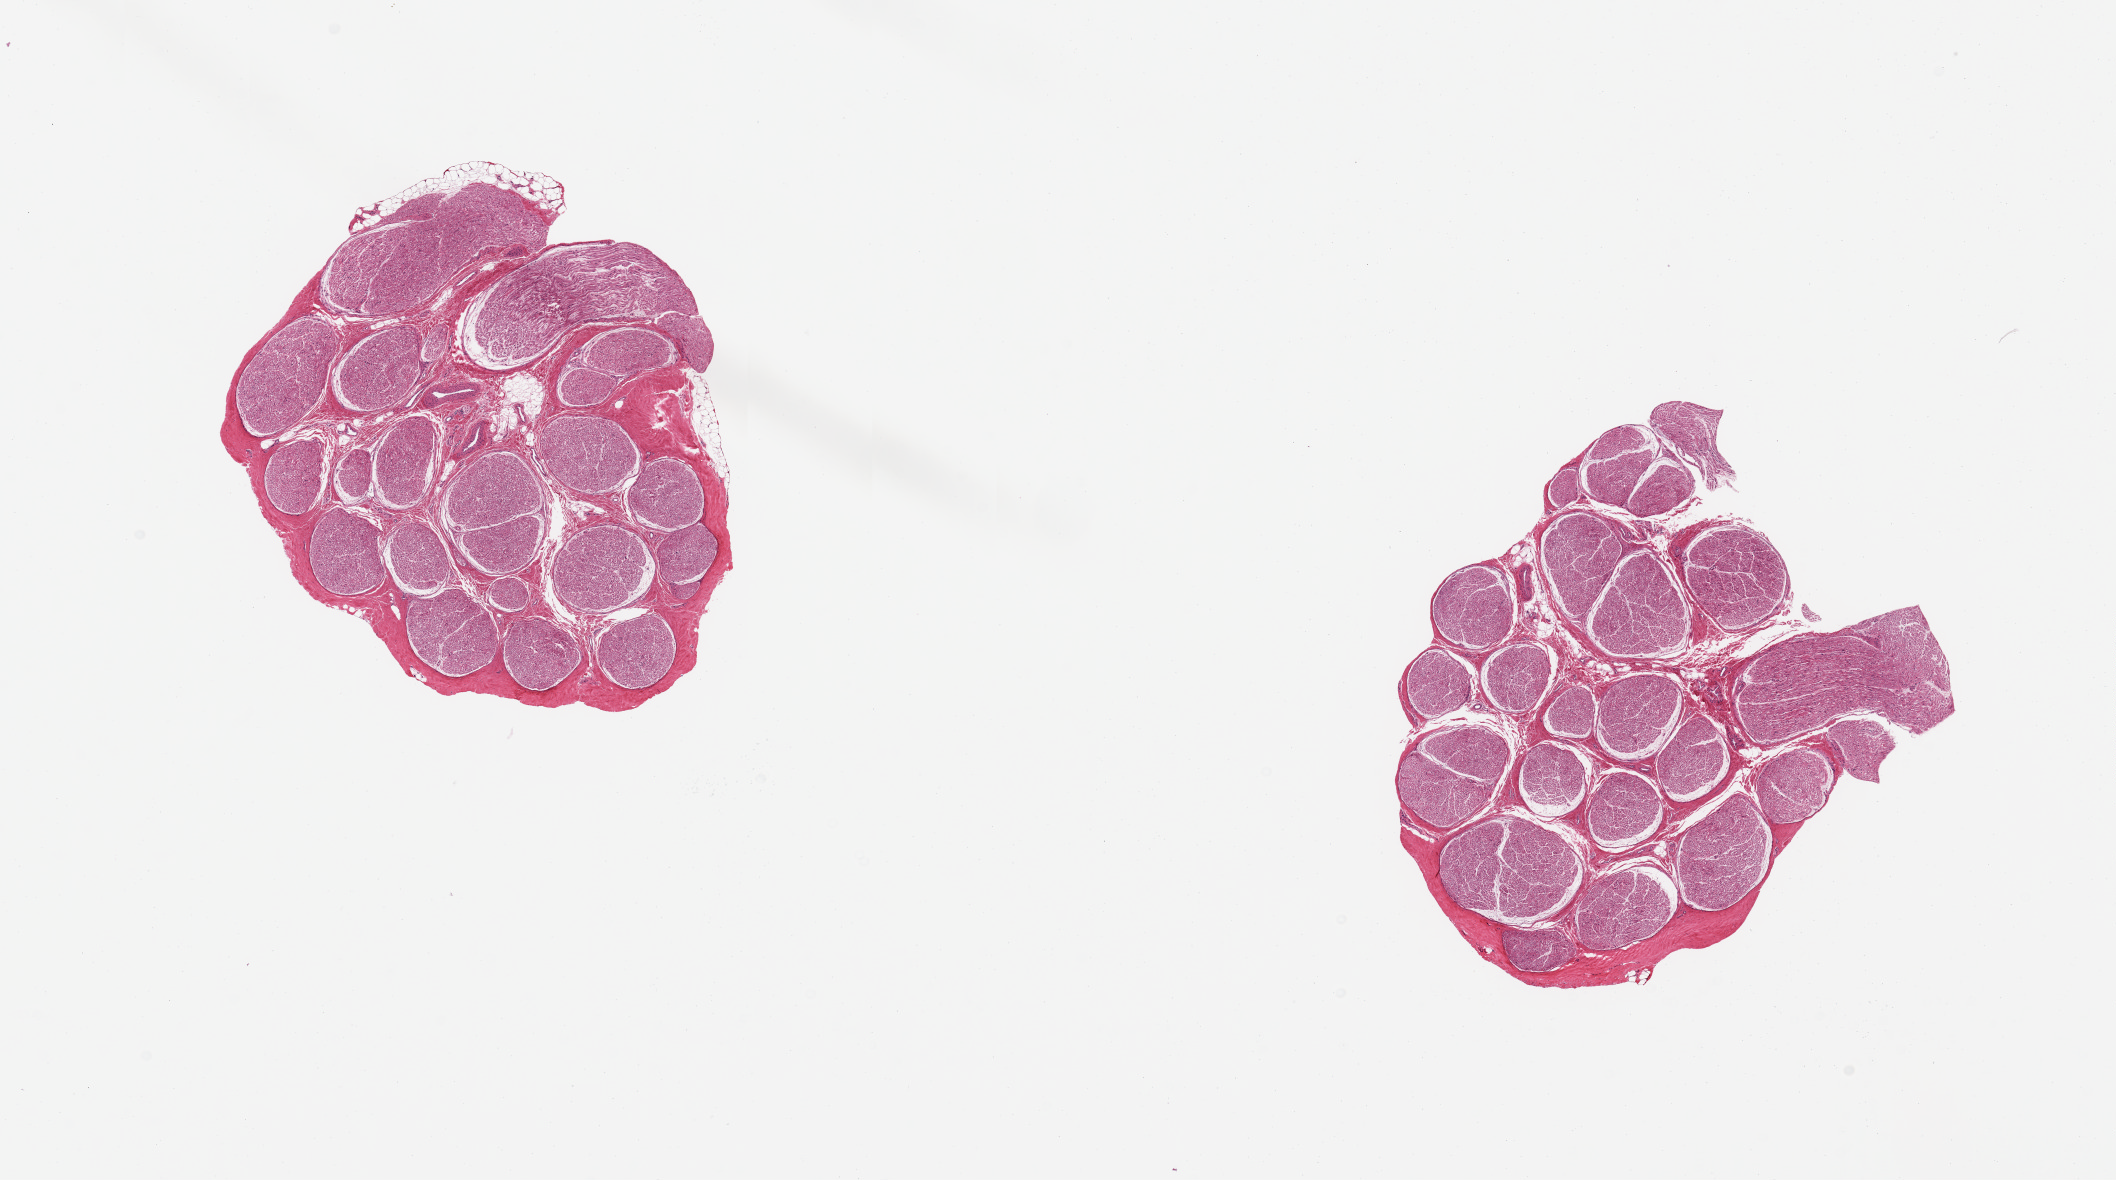
H&E whole-slide image, a low-resolution overview of the entire scanned area, about 16.7 x 9.3 mm. PAXgene-fixed, paraffin-embedded tissue. Section of tibial nerve (target tissue). Donor tissue sample. Donor sex: male.
Pathologist's review note for this sample: 2 pieces; well trimmed with scant attached fat.